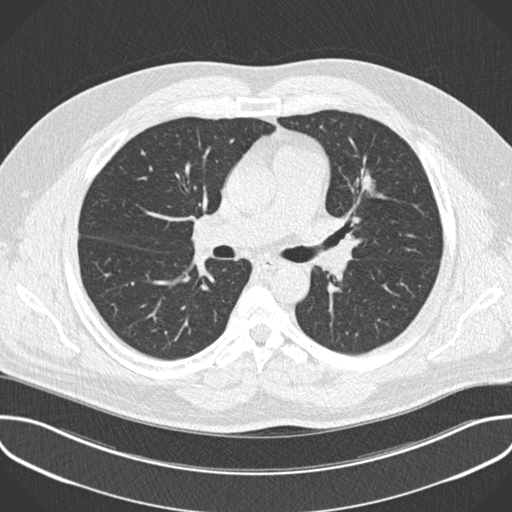
Low-dose screening chest CT, one axial slice; slice 128 of 201 in the series (ordered by position); 120 kVp; lung window (W 1500 / L -600 HU); 2 mm slice thickness; 512 × 512 image matrix, field of view 386 × 386 mm.
Outlined on this slice (outlined manually by an expert reader):
- lesion 1 (tumor, upper lobe of left lung): bounding box <357,169,373,190> (left, top, right, bottom; pixels)